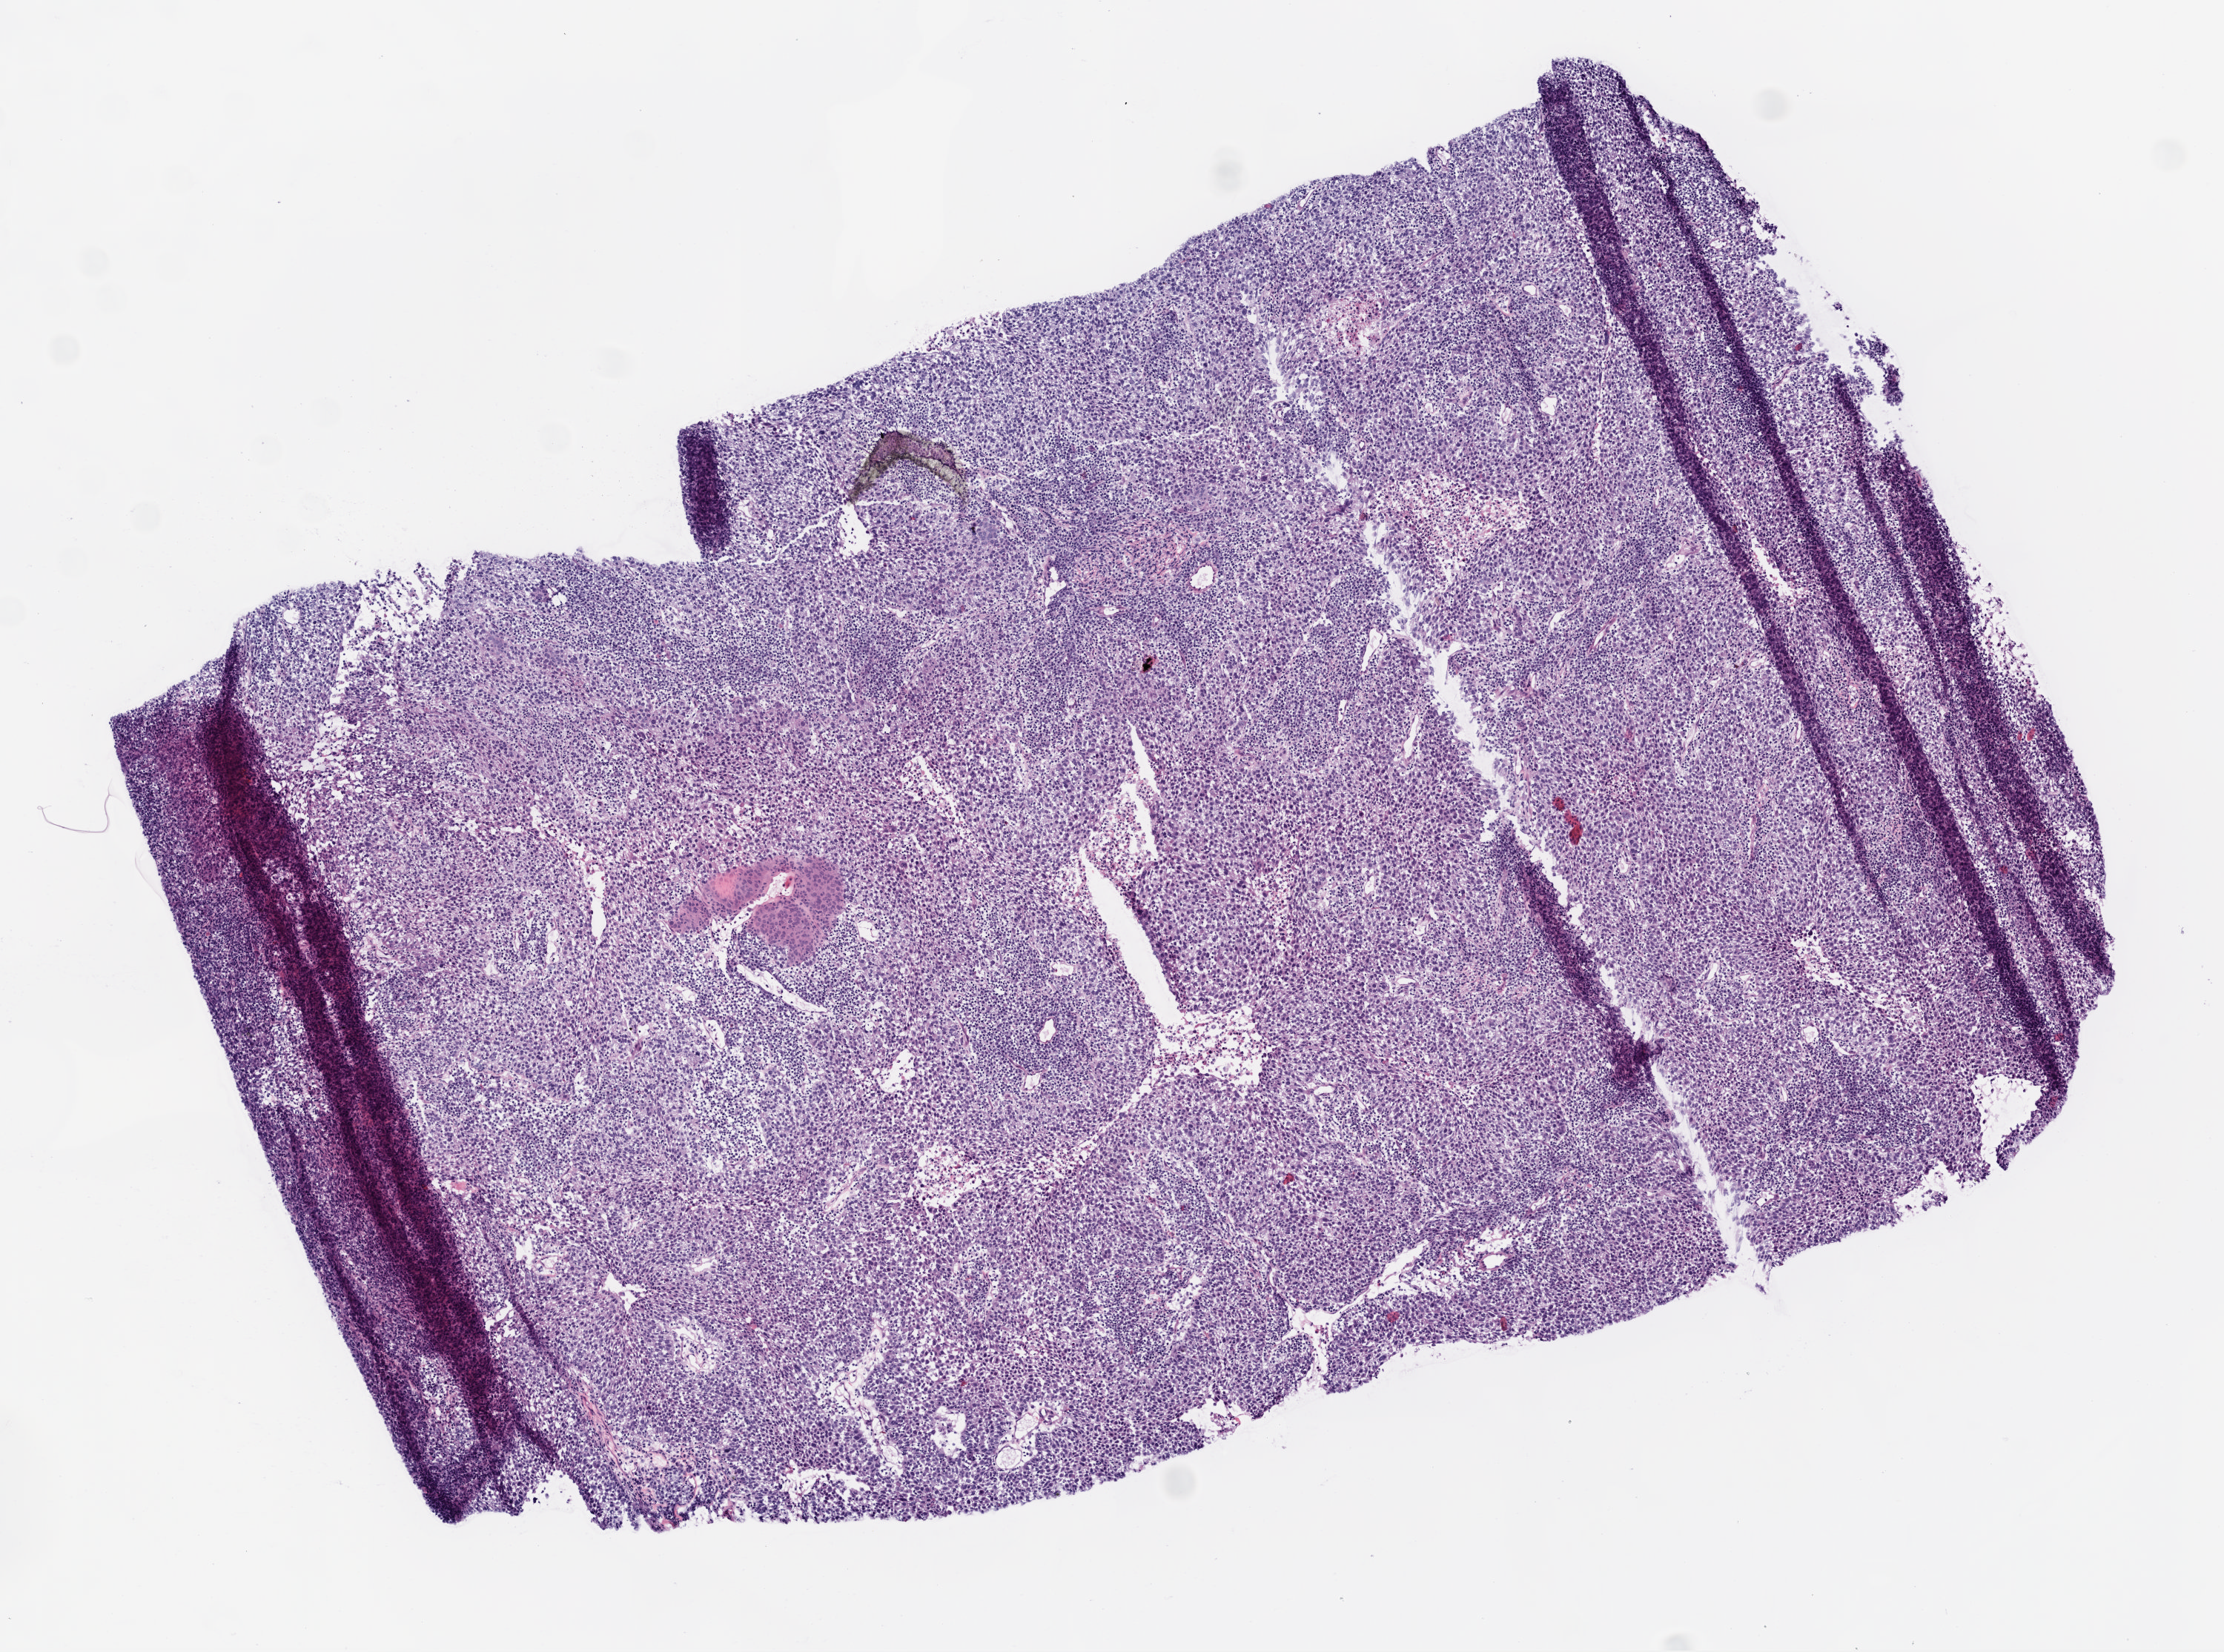
Digitized H&E tissue section (whole slide) — shown as a low-resolution overview of the whole scanned area (about 6.0 x 4.5 mm, slide scanned at 20x), frozen section from the top of the tissue portion, primary tumour sample from the lung. Male, age 83 years at initial diagnosis. Pathologist review of this section (percent, as recorded): tumour cells 90%, tumour nuclei 70%, normal cells 0%, stromal cells 7%, necrosis 3%. Infiltration values recorded for this section: lymphocyte infiltration 25%.
Diagnosis: Squamous cell carcinoma, NOS (upper lobe, lung). AJCC pathologic stage: IIB.